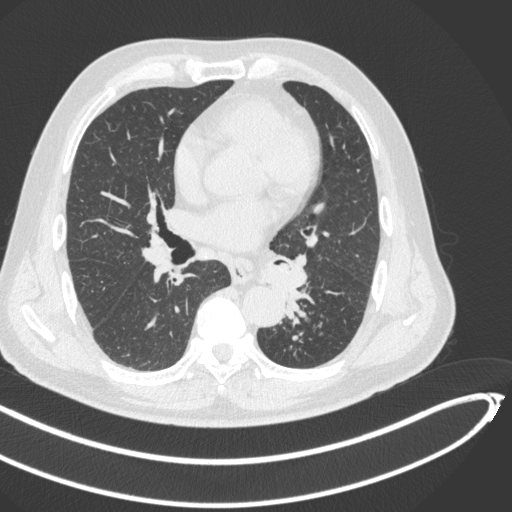
Chest CT, one axial slice; position 240 of 466 along the scan axis; reconstruction kernel B31f; lung window (W 1500 / L -600 HU); 1 mm slice thickness; 512 × 512 image matrix, field of view 400 × 400 mm. Male patient, age 64 years. Case-level facts recorded for this patient, not image findings: clinical TNM (as recorded): T1c N0 M0; histopathological grade: G2.
Structures marked on this image (bounding box drawn by a radiologist):
- lung tumour (recorded histology: squamous cell carcinoma): box from (x=263, y=261) to (x=300, y=299) px